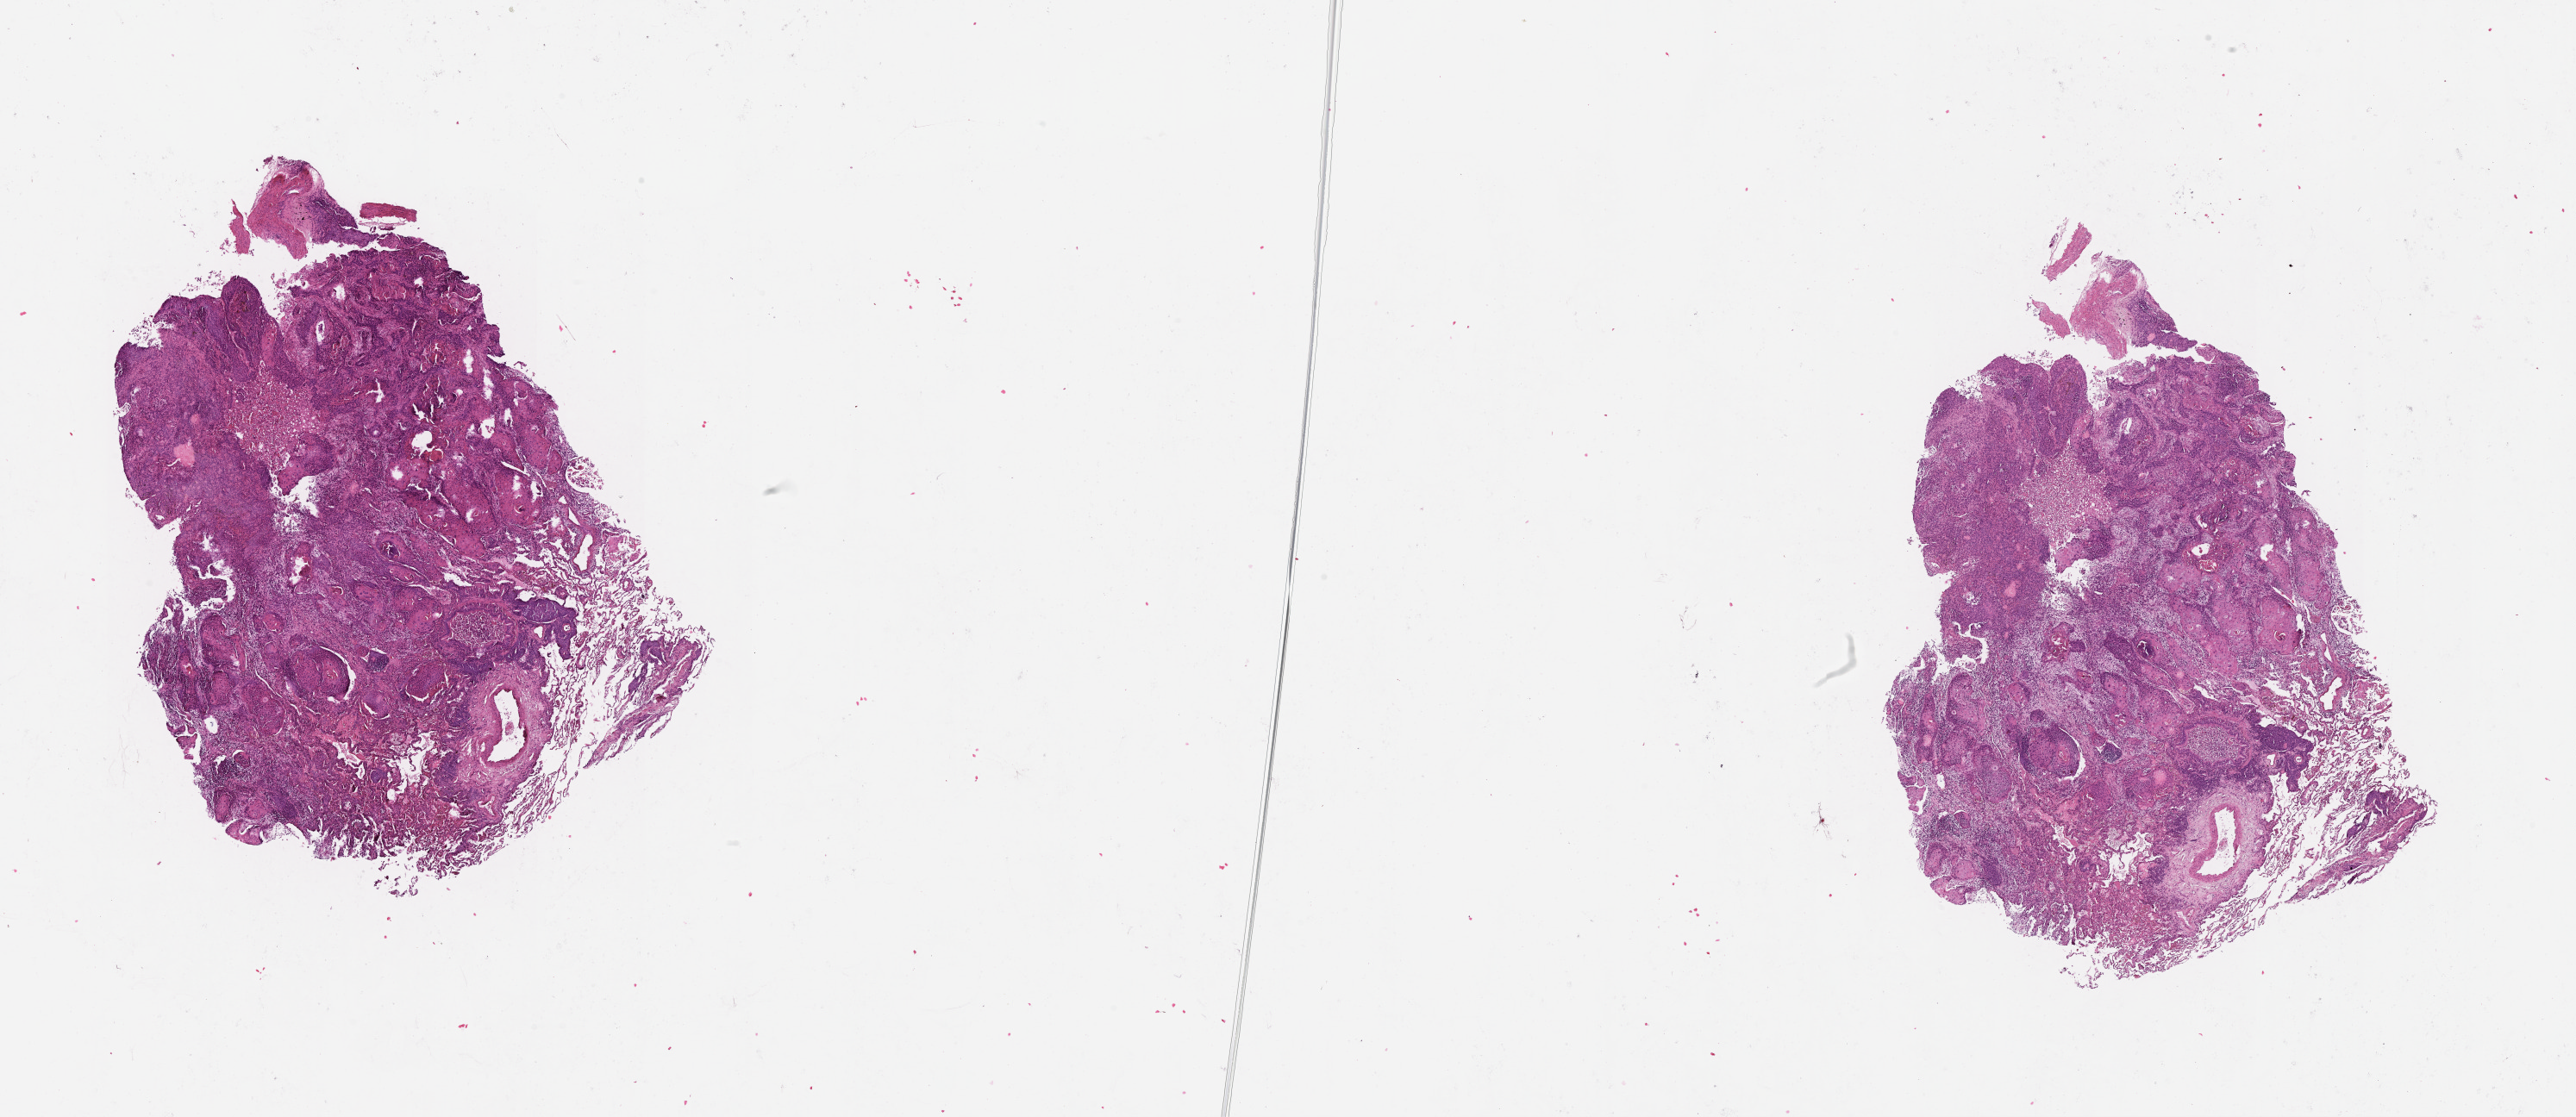
Hematoxylin and eosin (H&E) stained whole-slide image — low-resolution overview of the scanned area, about 24.1 x 10.4 mm (acquisition: 20x scan); tumour tissue sample, lung. Patient: male, age 80 years.
Patient diagnosis (cohort enrolment): squamous cell carcinoma (lung).